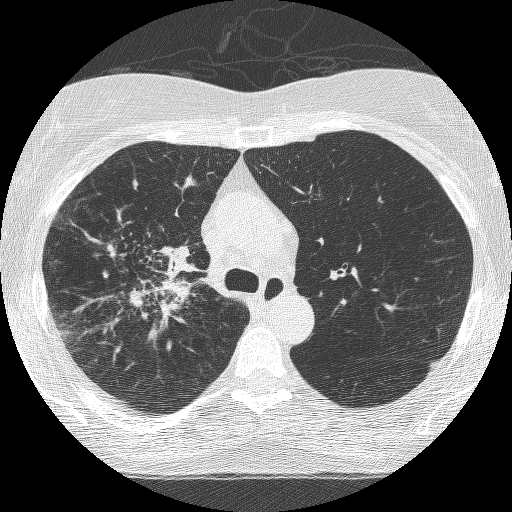
Axial slice from a low-dose chest CT screening exam. Third annual screen. Lung window (W 1500 / L -600 HU). 1.25 mm slice thickness. Slice 180 of 253 in the series. 512 × 512 image matrix, field of view 294 × 294 mm. Female participant, aged 64 years at enrolment. Former smoker at enrolment.
Lesion marked by an expert reader, bounding box [x1, y1, x2, y2] px = [93, 227, 207, 340]. Screening reader's record for this exam (one nodule recorded; not confirmed to be the boxed lesion): non-calcified nodule or mass ≥4 mm, right upper lobe, 49 × 43 mm, spiculated (stellate) margins, soft tissue attenuation, pre-existing on the prior screen: yes; interval growth: yes. Later outcome: lung cancer diagnosed 7 days after this screen — adenocarcinoma, NOS, right upper lobe, right middle lobe, right hilum, stage IV (AJCC 6th edition), 85 mm at pathology.